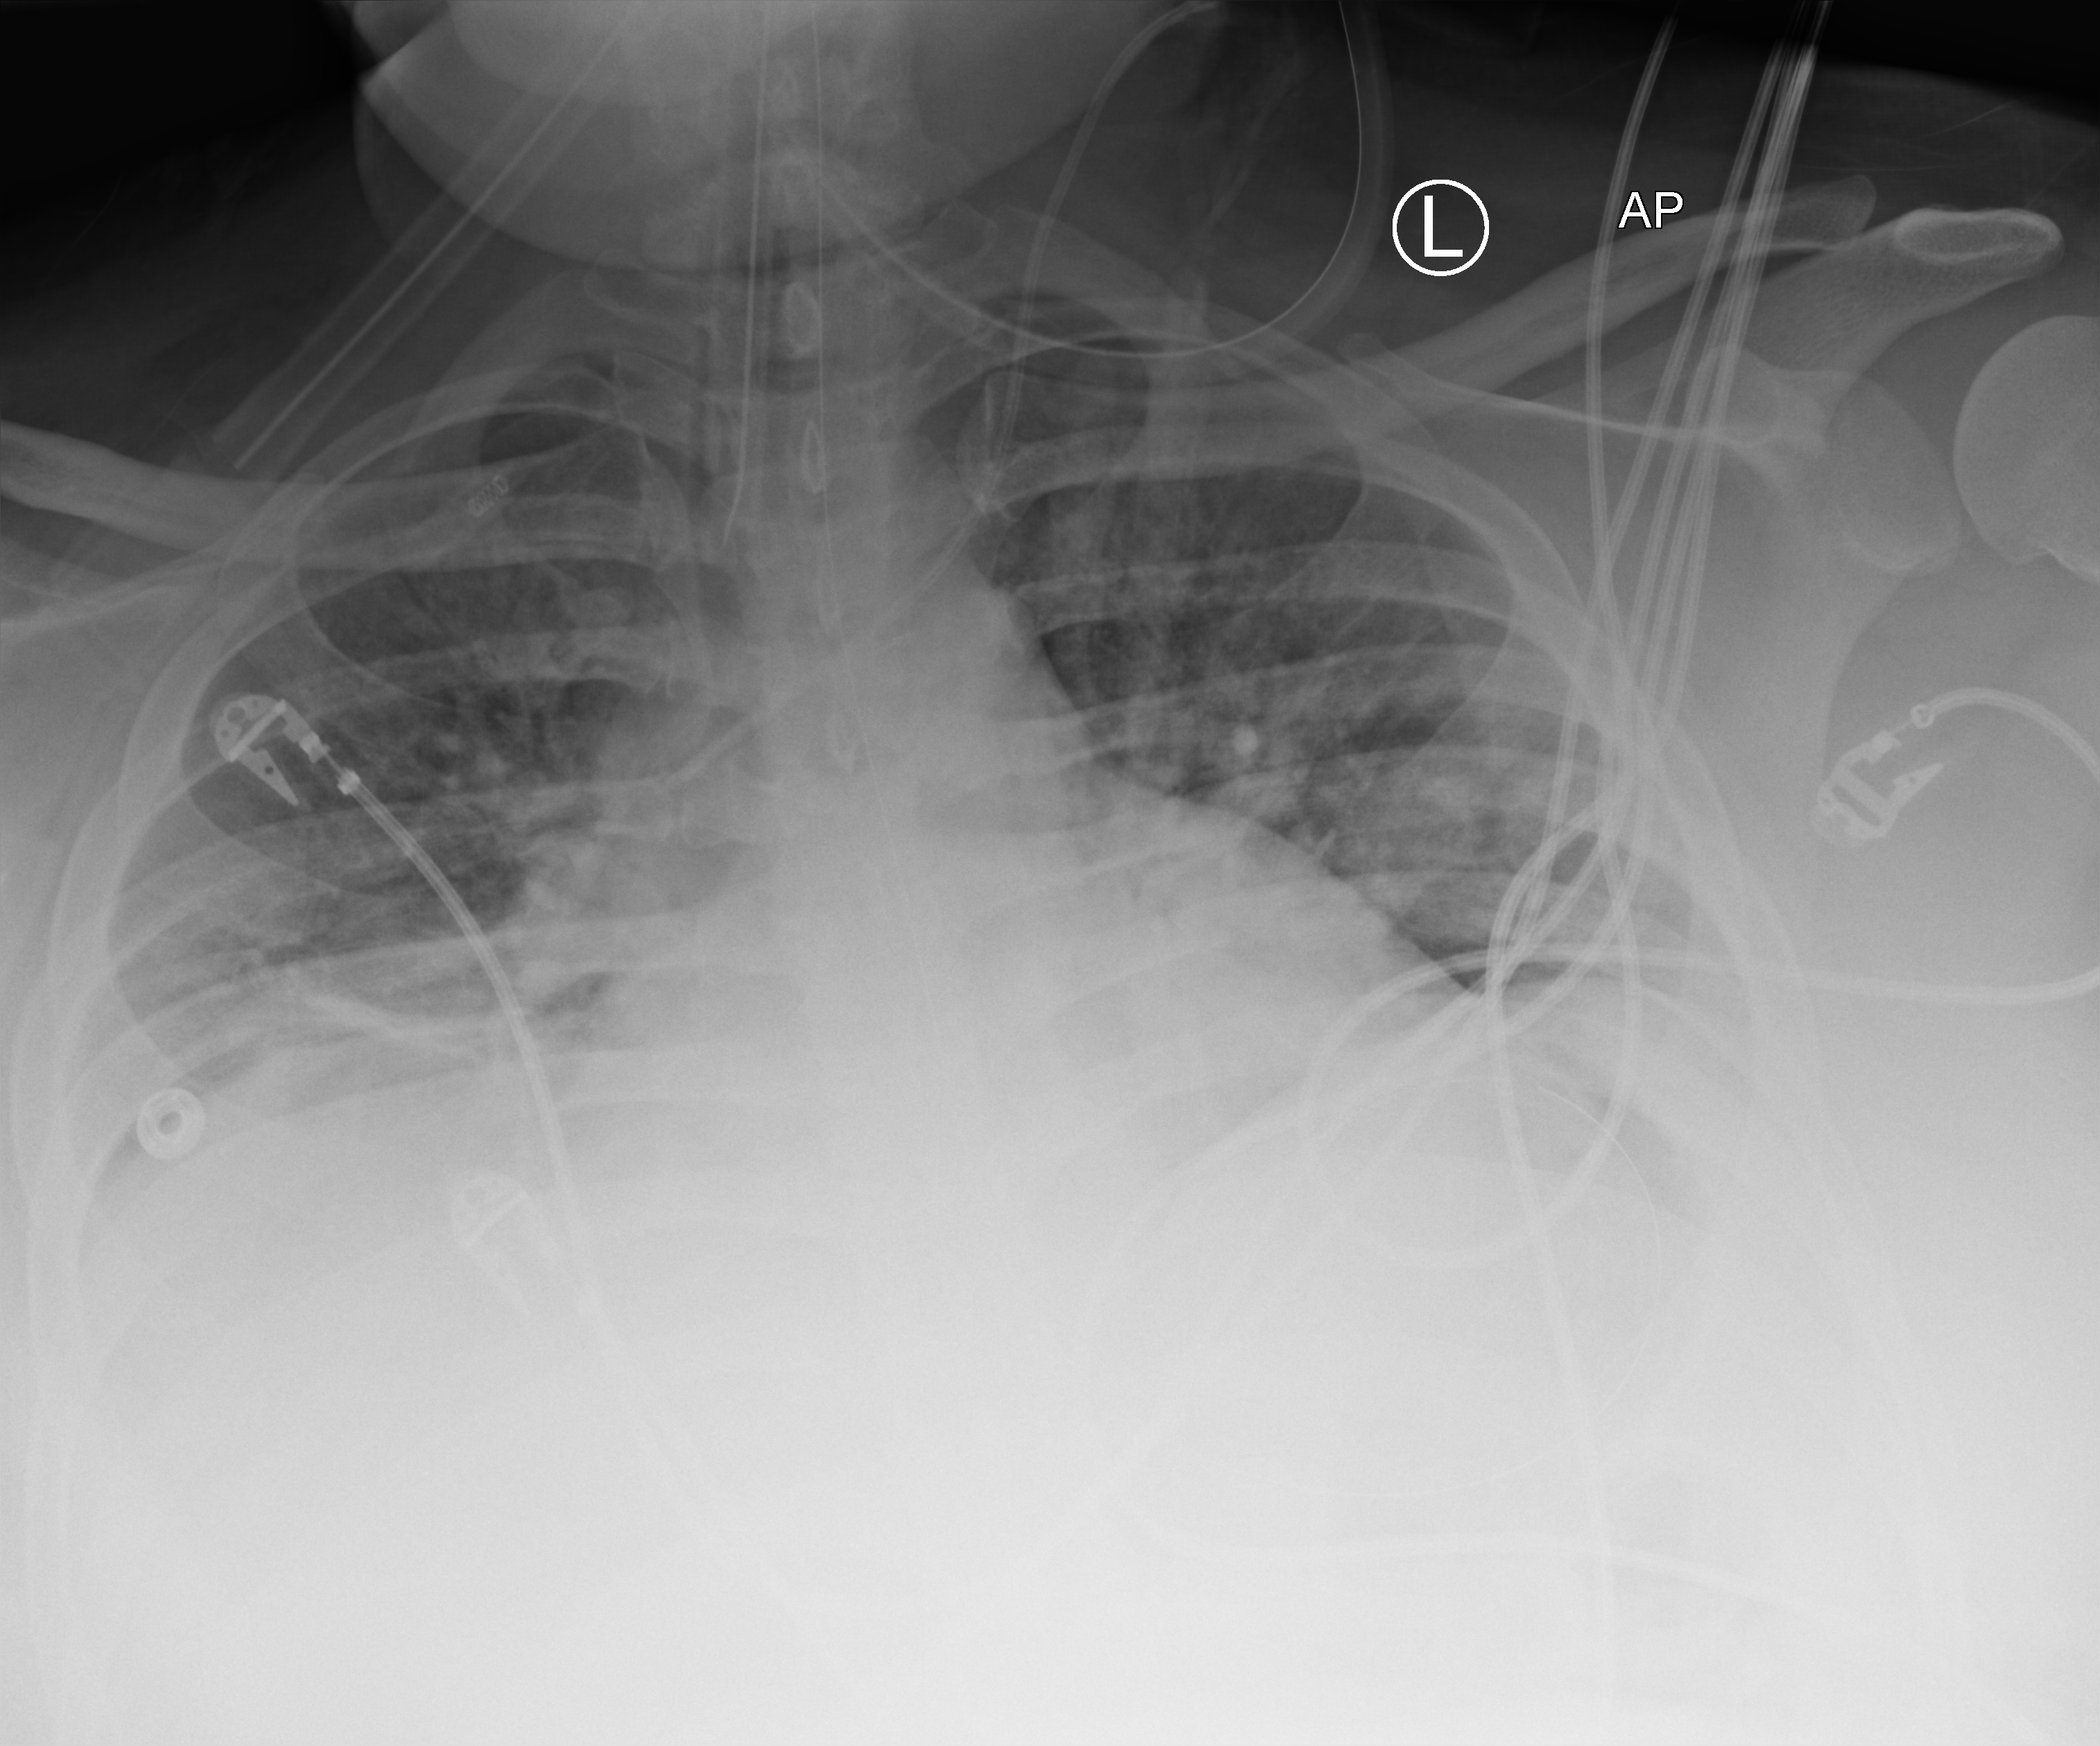
Portable chest radiograph, anteroposterior (AP) projection. Male patient hospitalised with COVID-19, age 18–59 years.
Admission-level facts for this patient (not findings on this image; timing relative to this image not recorded): length of hospital stay: 69 days; admitted to intensive care during this hospital stay: yes.